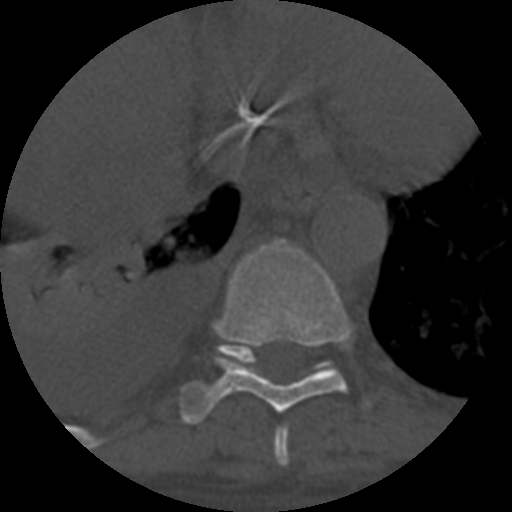
CT including the spine, one axial slice. Slice 375 of 708 in the series (ordered by position). Reconstruction kernel STANDARD. One of 3 acquisitions stored at this slice position. Bone window (W 1800 / L 400 HU). 512 × 512 image matrix, field of view 160 × 160 mm. Patient age 55 years. Case-level facts recorded for this patient, not image findings: primary cancer: colon; vertebrae with lytic lesions (as recorded): T12, L1, L5.
Outlined on this slice (semi-automatic segmentation, software-assisted and operator-edited):
- T10 vertebra: bounding box (x1, y1, x2, y2) in pixels: (221, 344, 333, 370)
- T8 vertebra: (274, 425, 289, 467)
- T9 vertebra: (183, 240, 352, 425)